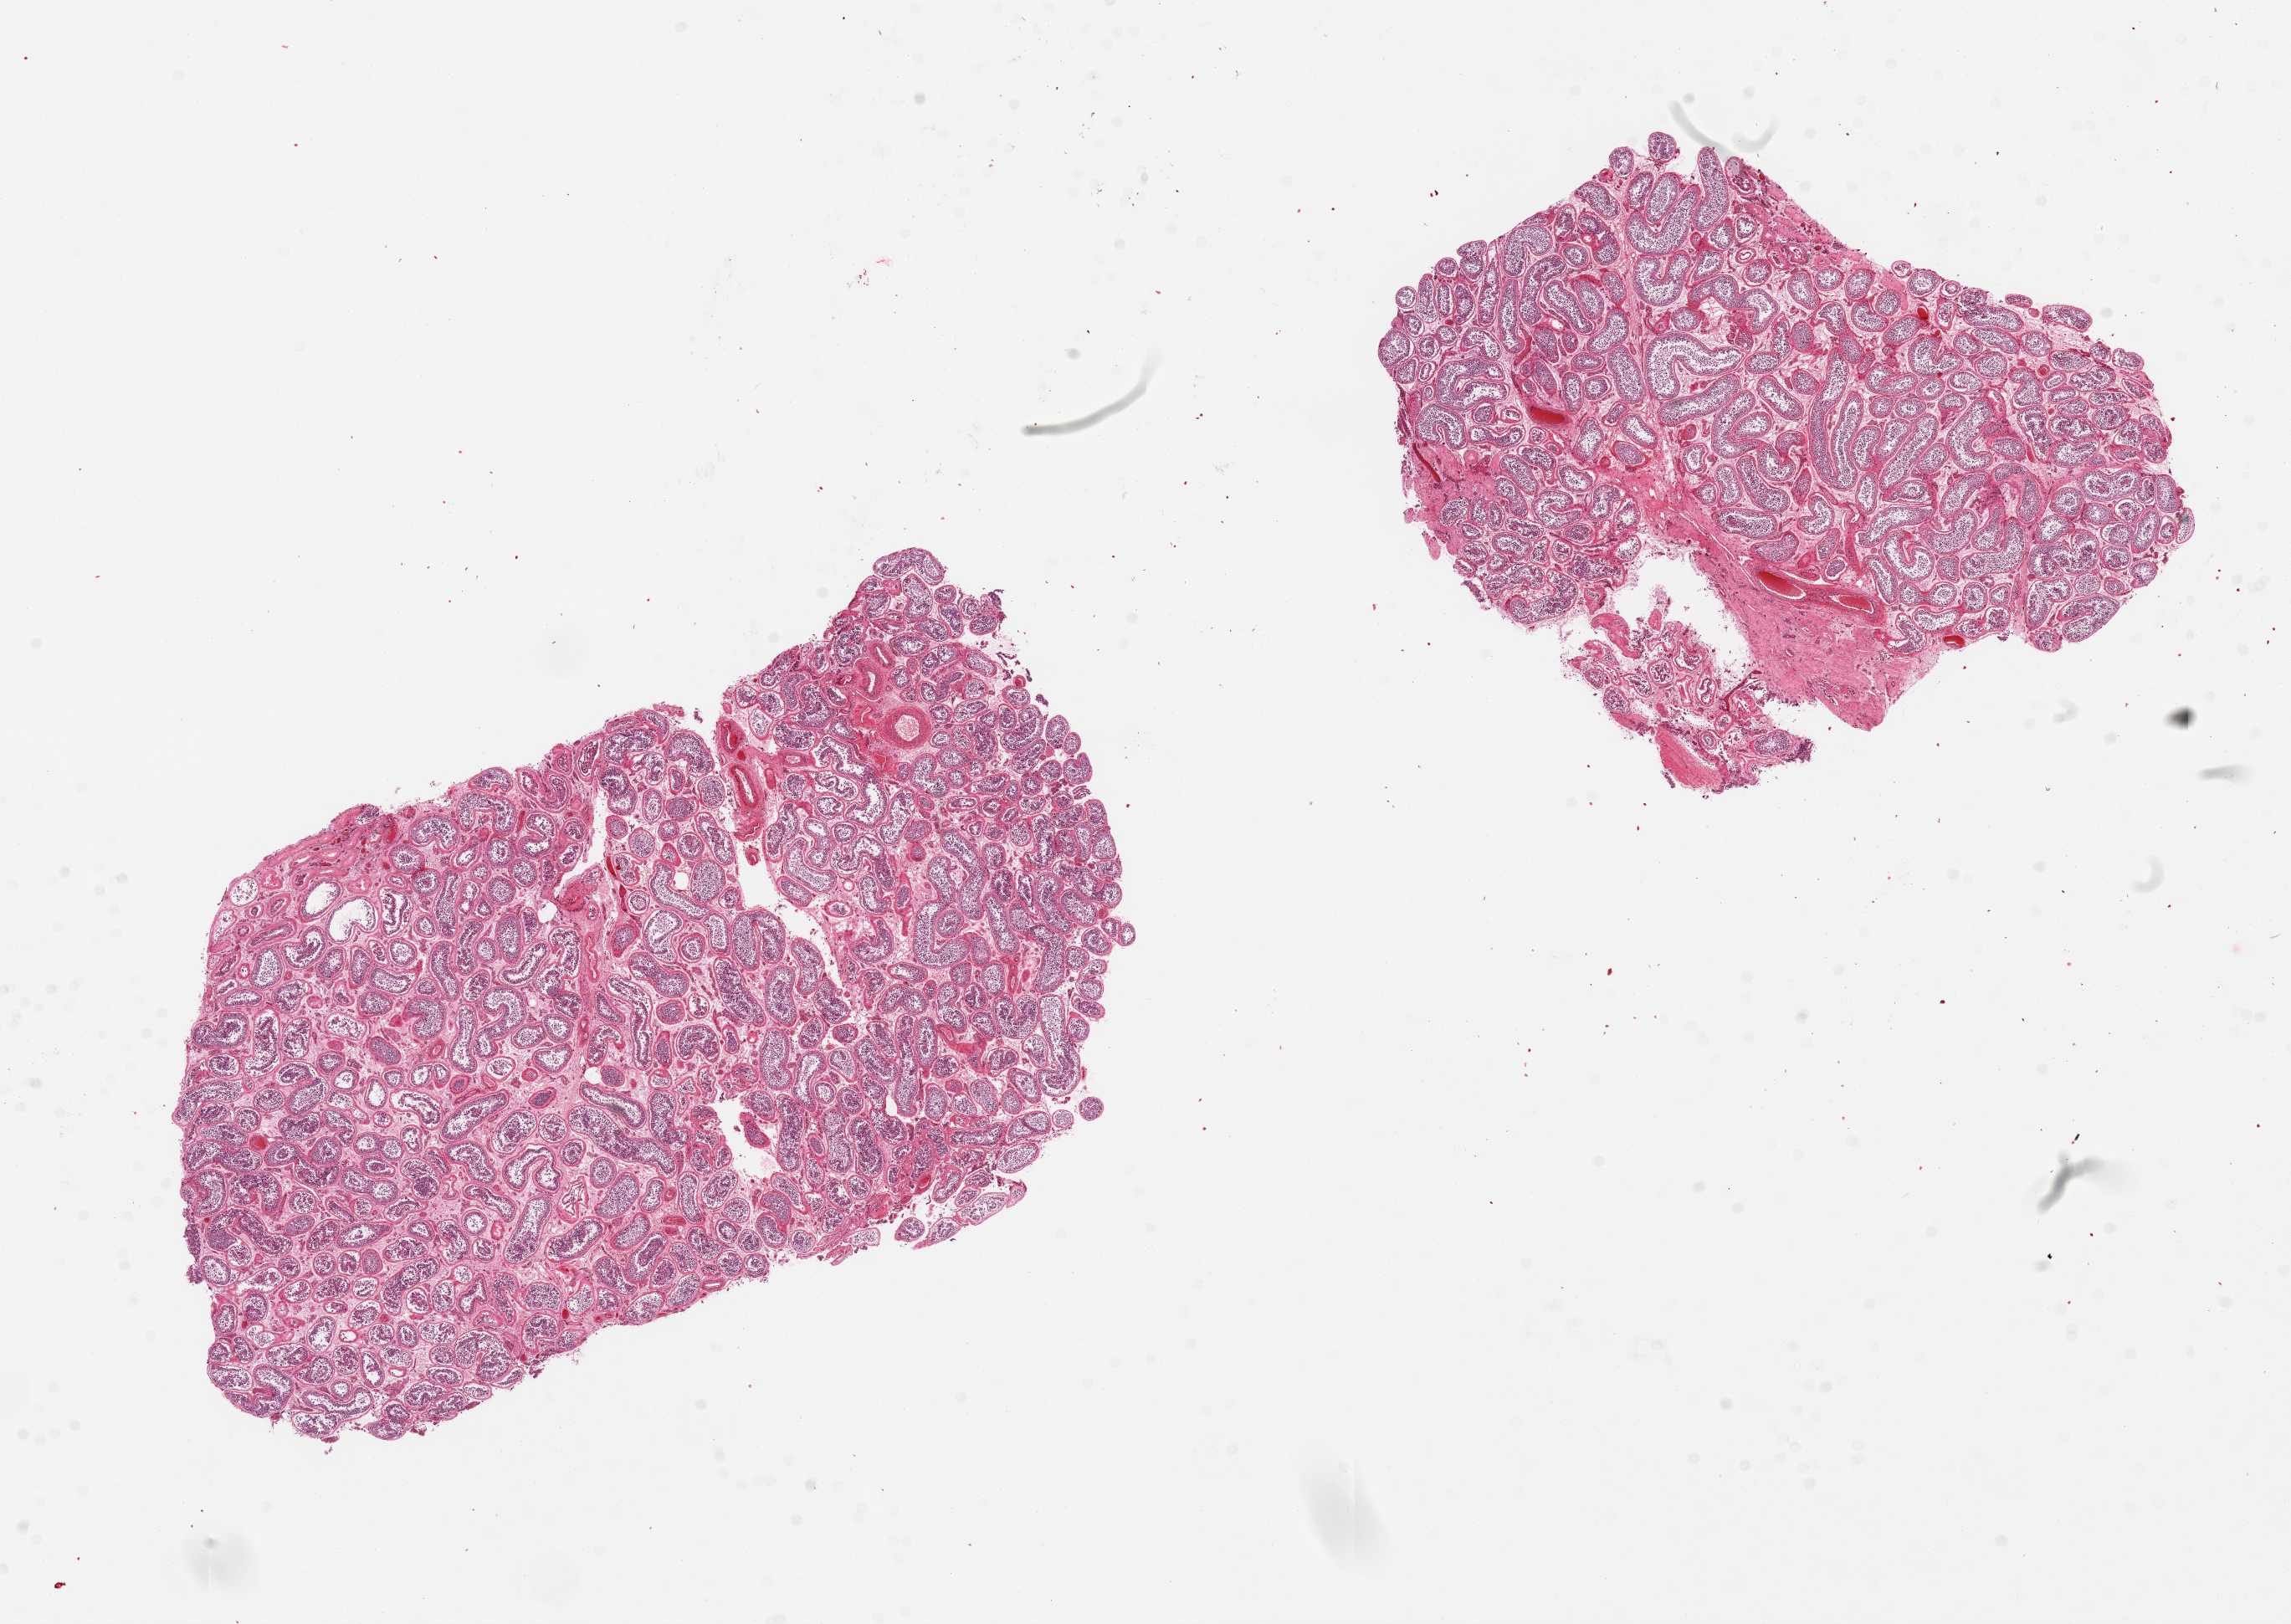
Digitized hematoxylin and eosin (H&E)-stained section — whole scanned area (about 21.7 x 15.4 mm, slide scanned at 20x) shown as a low-resolution overview. PAXgene-fixed paraffin-embedded (PFPE) section. Target tissue: testis. Tissue donor sample. Male donor.
* pathologist's review note for this sample: 2 pieces, active spermatogenesis, peritubular fibrosis and focal tubular hyalinization